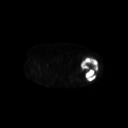
FDG PET of an extremity soft-tissue mass (from a PET/CT study), one axial slice; 3.27 mm slice thickness; 128 × 128 image matrix, field of view 700 × 700 mm. Female patient, age 62 years. Case-level facts recorded for this patient, not image findings: histological type: undifferentiated – high grade; grade: high; site of the primary tumour: left thigh.
Annotated regions visible in this slice (expert contour drawn on MRI and transferred to this co-registered scan by the dataset authors):
- gross tumour volume including surrounding oedema: bounding box [x1, y1, x2, y2] px = [81, 57, 98, 81]
- gross tumour volume (mass): [81, 57, 98, 81]